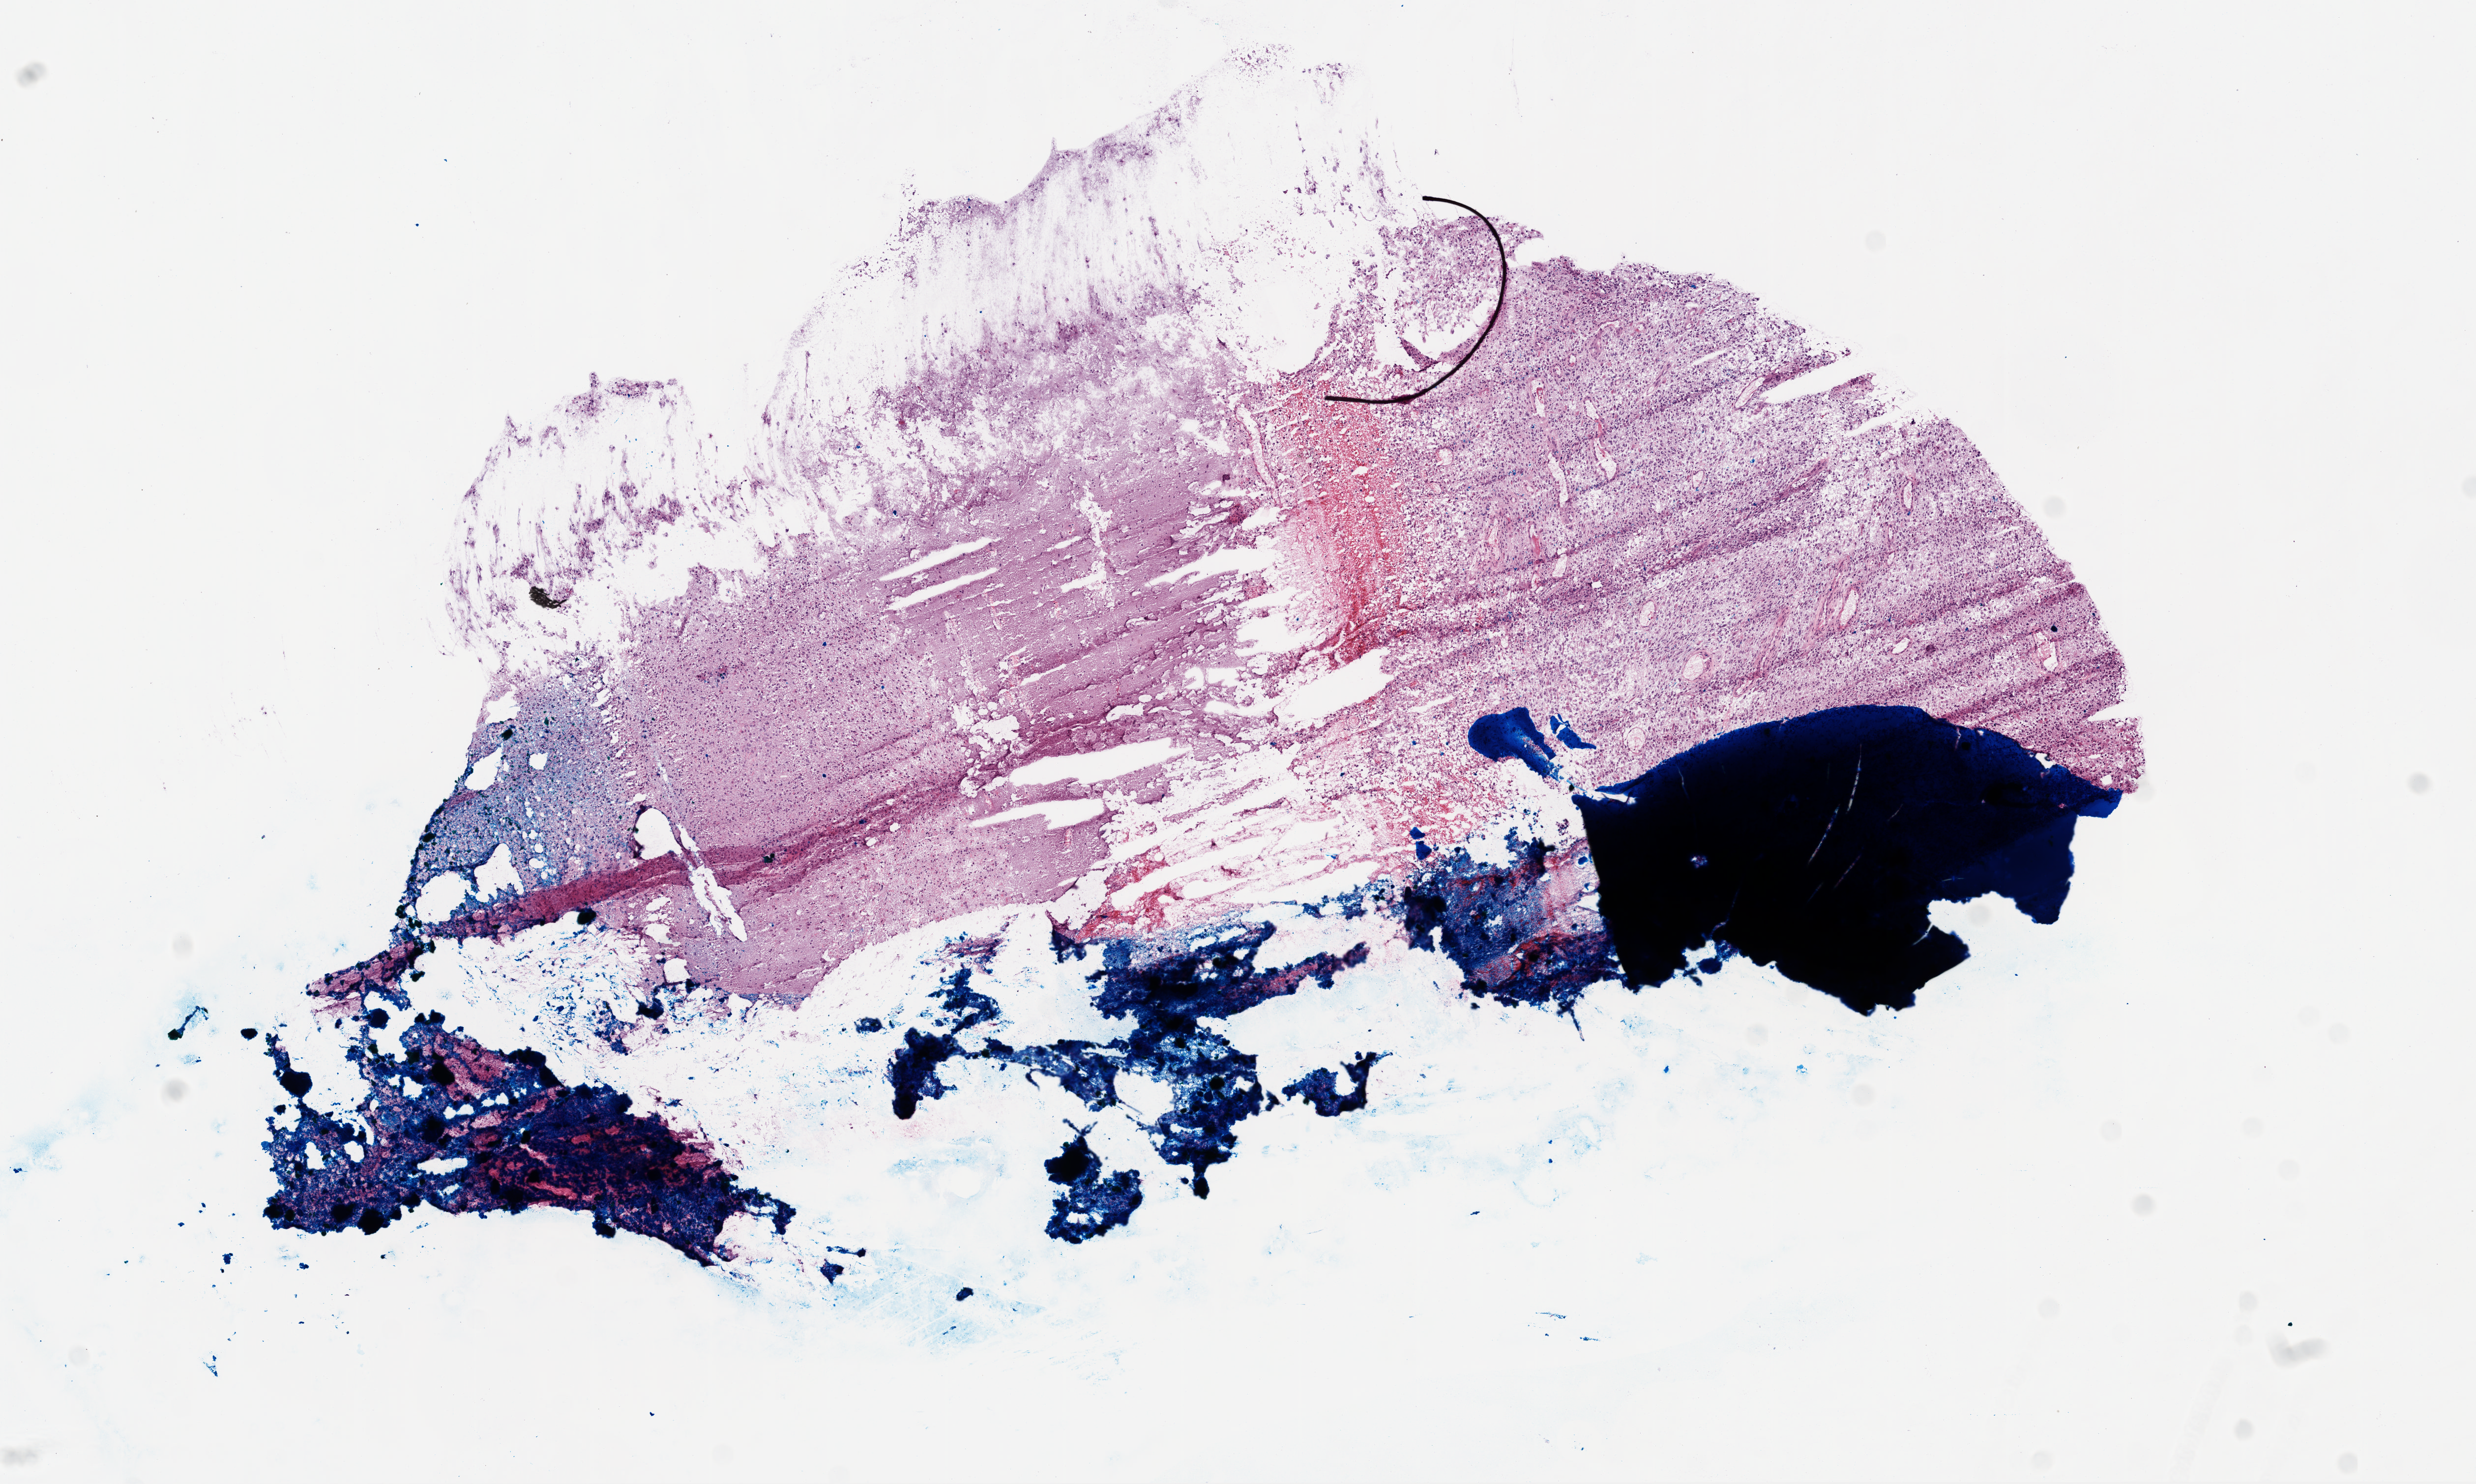
Hematoxylin and eosin (H&E) stained whole-slide image — low-resolution overview of the scanned area, about 10.2 x 6.1 mm, frozen section, primary tumour sample from the brain. Male, age 60 years at initial diagnosis. Pathologist review of this section (percent, as recorded): tumour cells 60%, tumour nuclei 90%, normal cells 0%, stromal cells 30%, necrosis 10%.
* histologic diagnosis: Glioblastoma